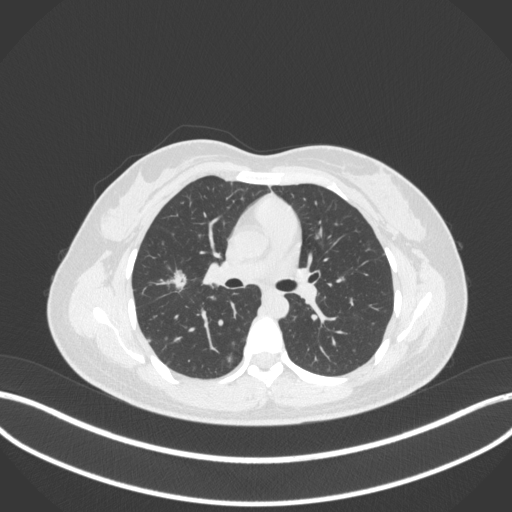
Chest CT, one axial slice. Position 197 of 214 along the scan axis. 120 kVp. Lung window (W 1500 / L -600 HU). 1 mm slice thickness. 512 × 512 image matrix, field of view 400 × 400 mm. Patient: female, 33 years. From the clinical record (not read from this slice): clinical TNM (as recorded): T1c N0 M0; histopathological grade: G2-G3.
Annotated regions visible in this slice (bounding box drawn by a radiologist):
- lung tumour (recorded histology: adenocarcinoma): box from (x=166, y=268) to (x=188, y=293) px